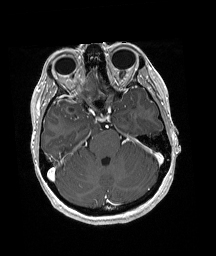
Brain MRI from a brain-tumour surgery series, one axial slice. Slice 127 of 192 in the series (ordered by position). T1-weighted post-contrast. 1 mm slice thickness. 216 × 256 image matrix. Case-level facts recorded for this patient, not image findings: histopathology: Oligodendroglioma; WHO grade: 3; IDH mutation: yes; tumour location: Right Frontal.
Annotated regions visible in this slice (outlined manually by an expert reader):
- tumour: box from (x=57, y=74) to (x=96, y=112) px